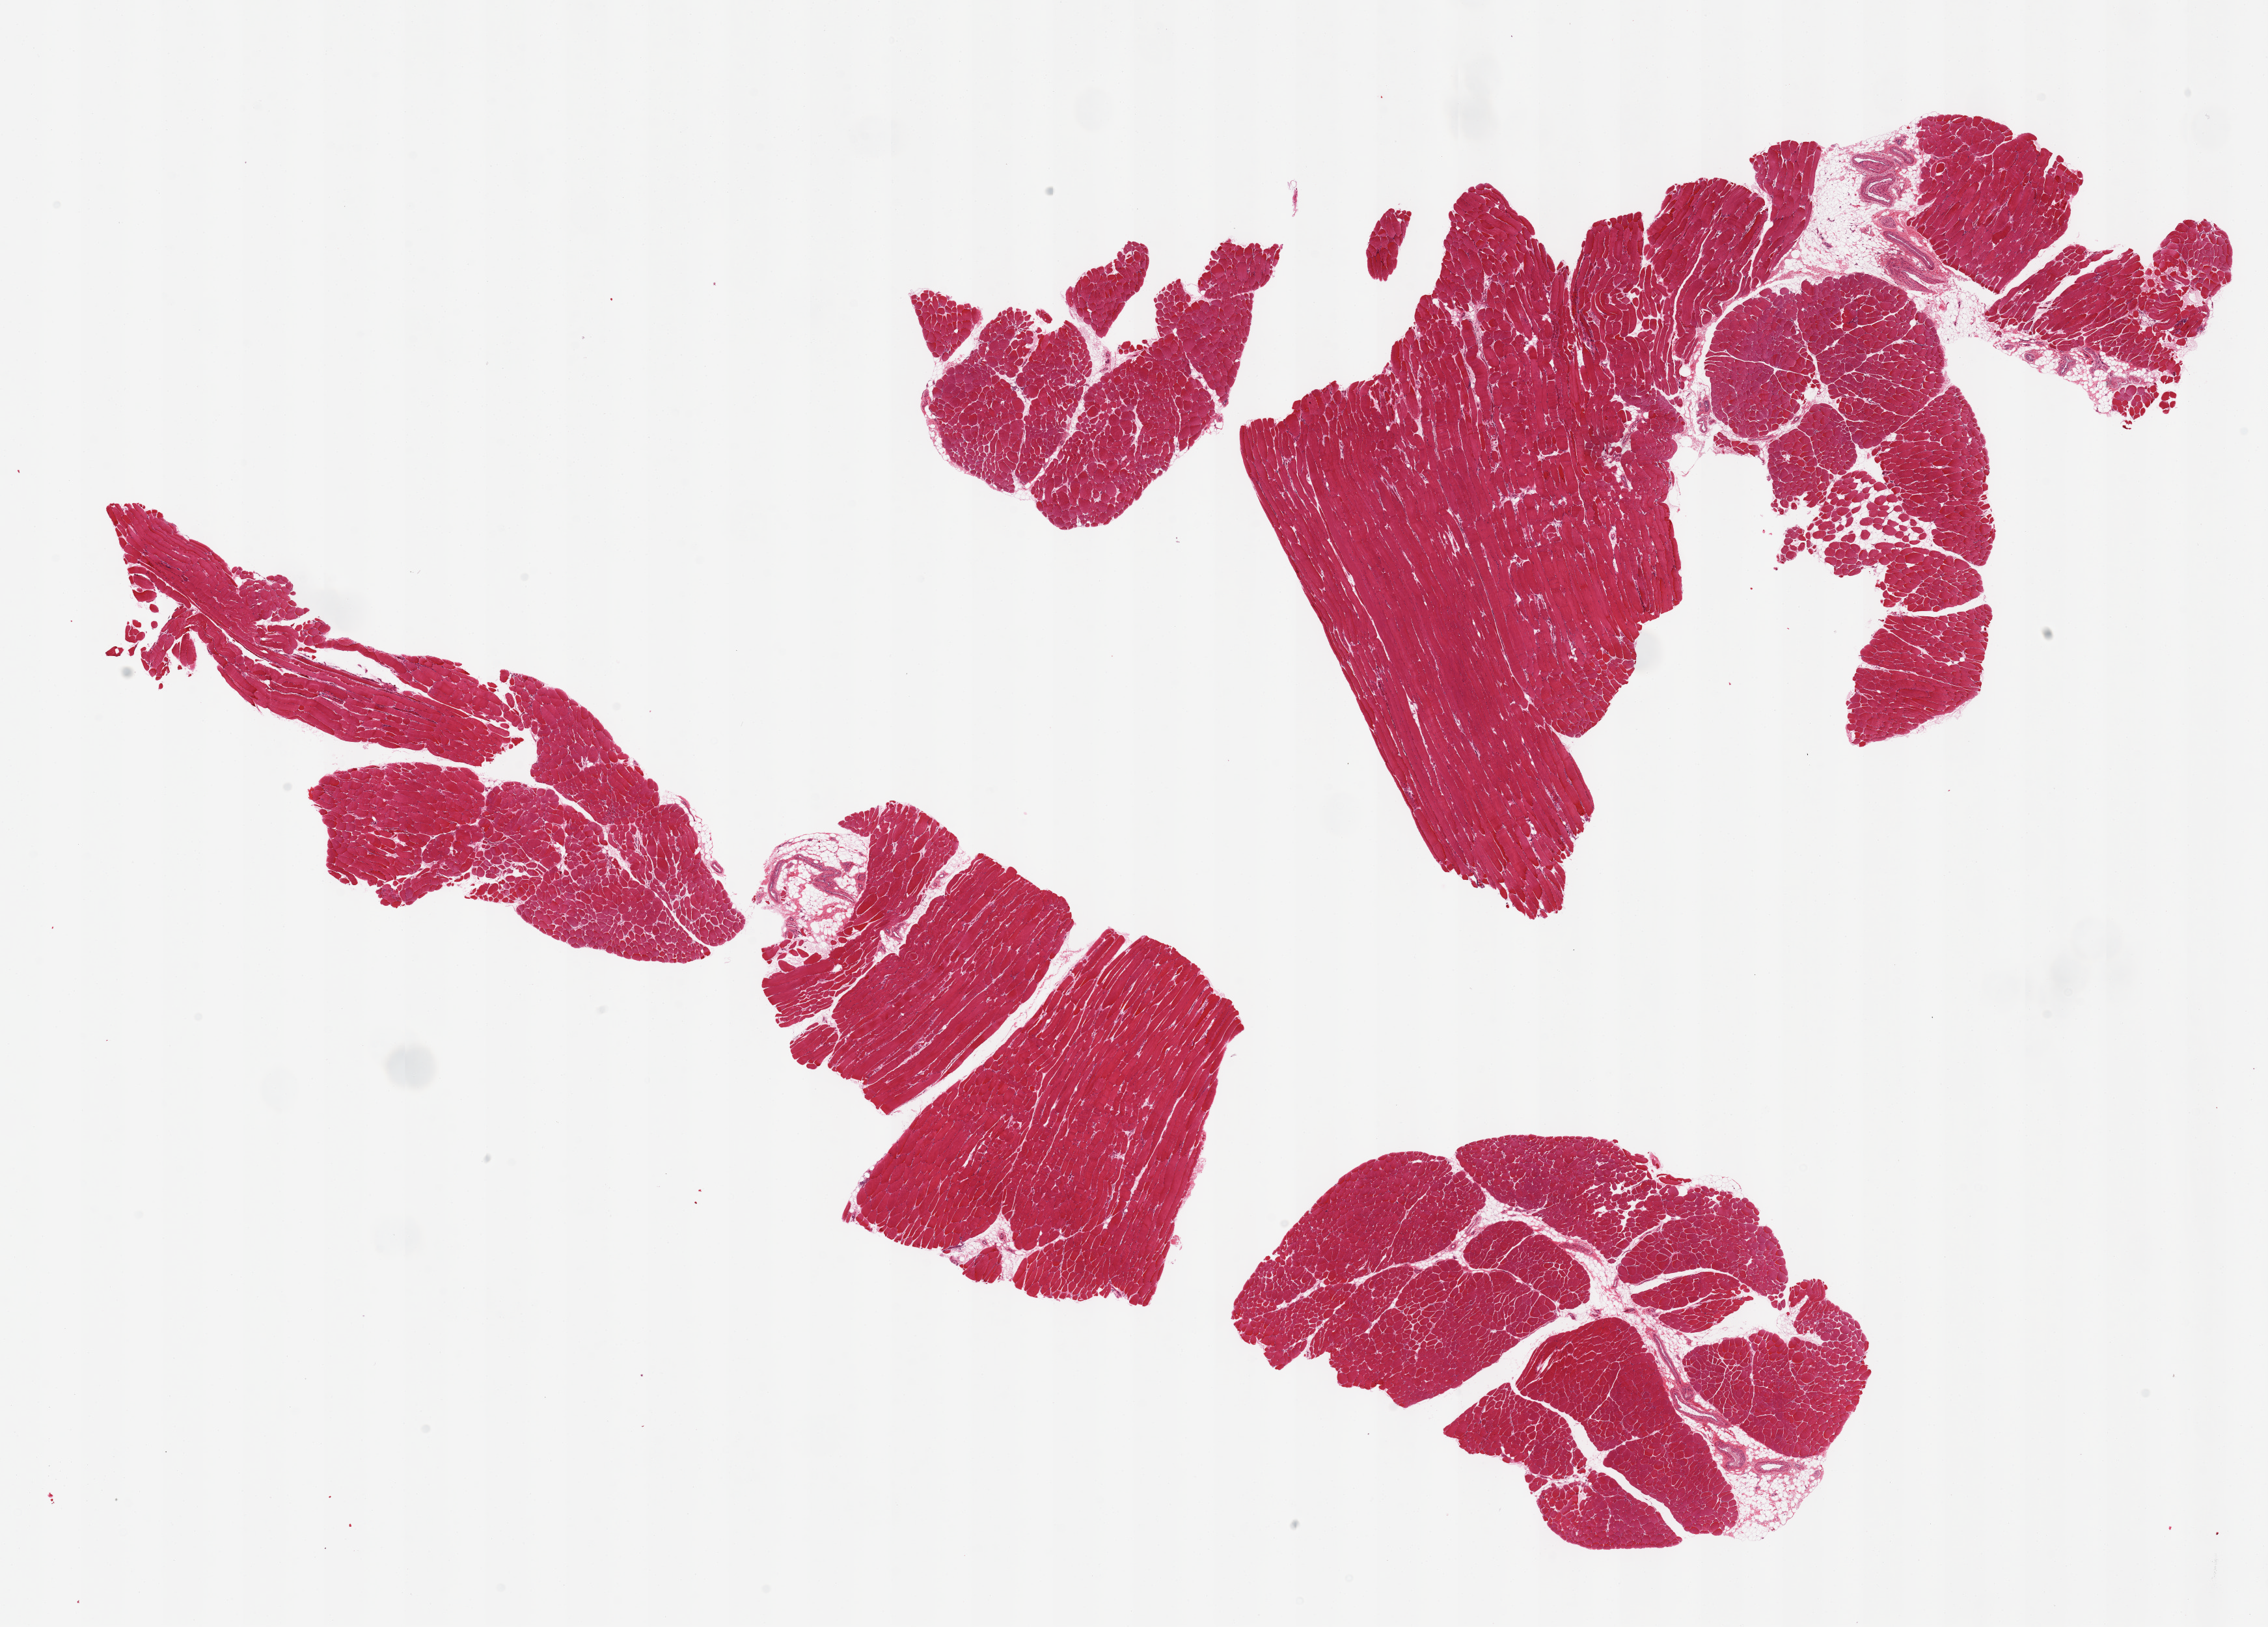
Digitized haematoxylin and eosin-stained section — low-resolution overview of the scanned area, about 27.6 x 19.8 mm, PAXgene-fixed, paraffin-embedded tissue, section of skeletal muscle (target tissue), donor tissue sample. Female donor.
Reviewer comment on this tissue sample: 2 pieces, but fragmented.